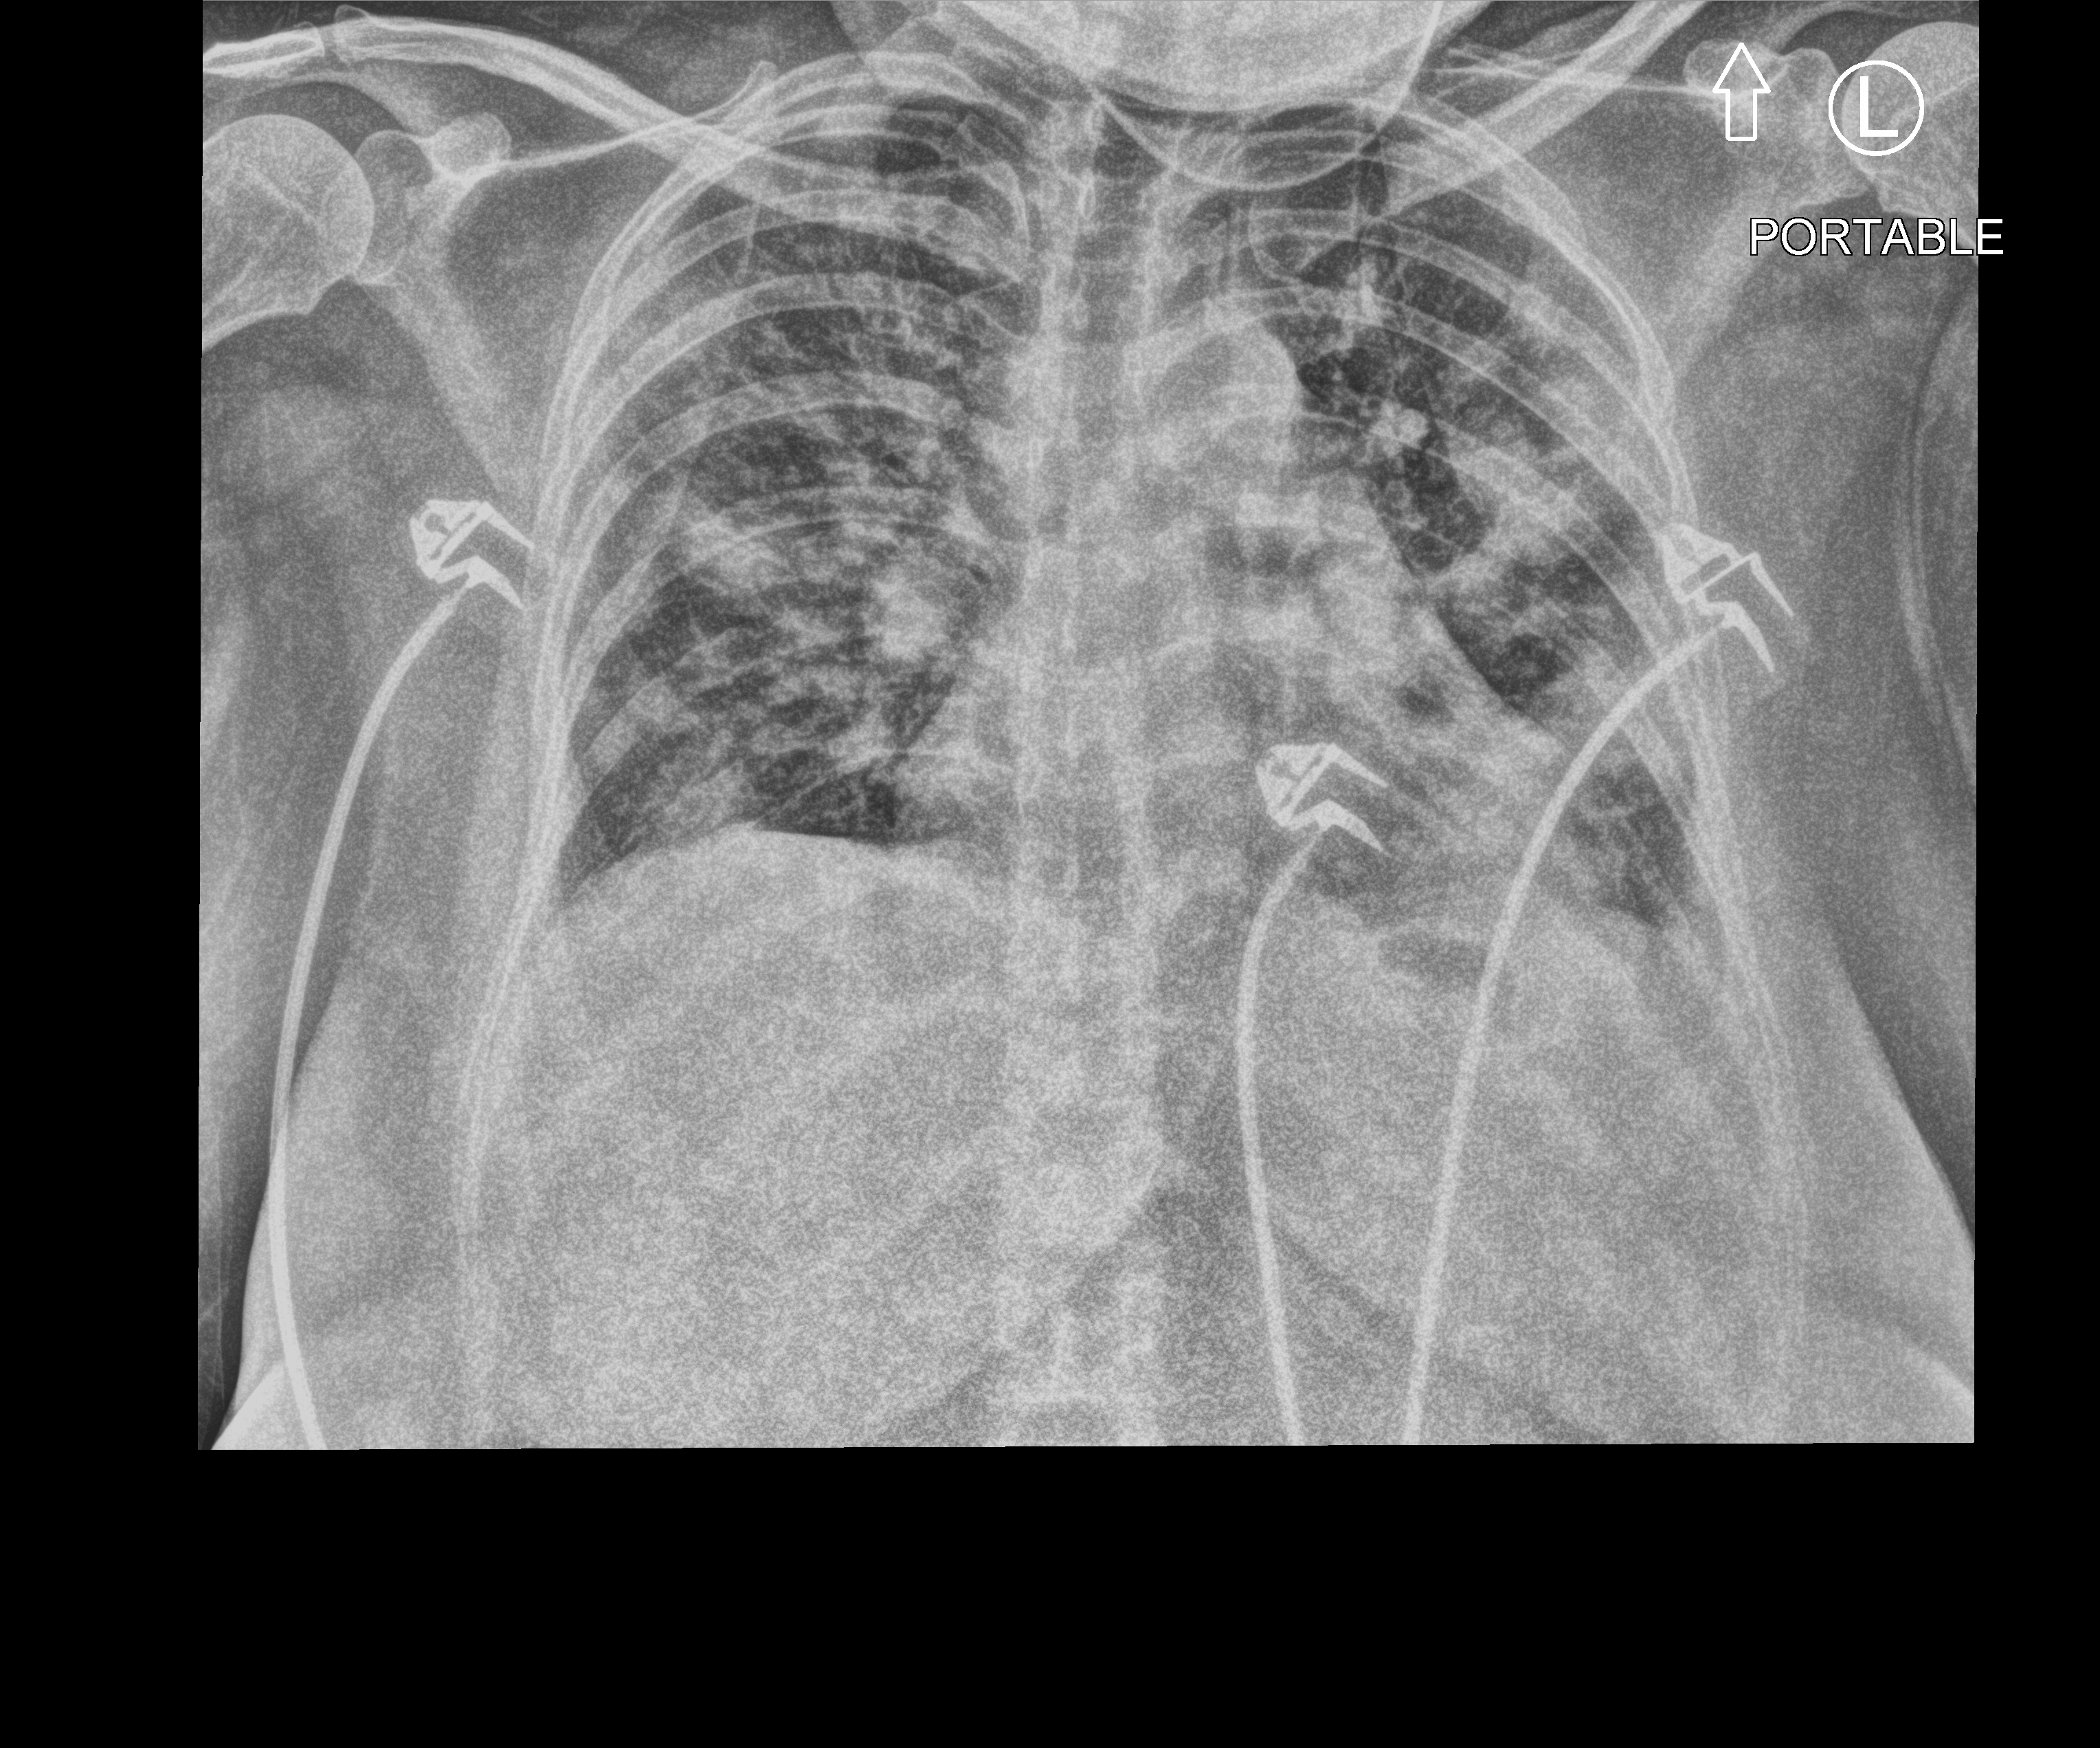
Chest X-ray (portable), anteroposterior (AP) projection. Adult patient hospitalised with COVID-19, age 18–59 years.
From the hospital-stay record, not from the radiograph (when in the stay this image was taken is not recorded):
- admitted to intensive care during this hospital stay: yes